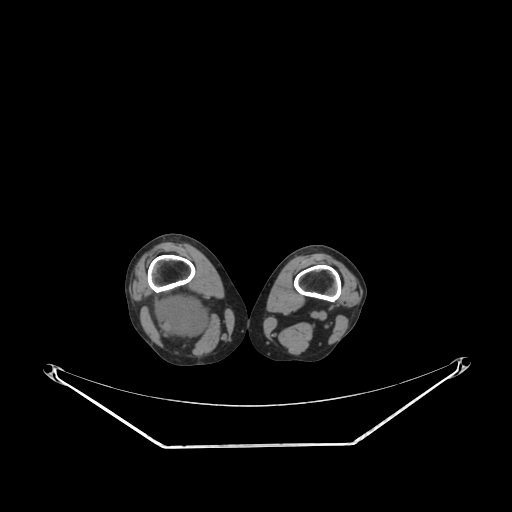
CT of an extremity soft-tissue mass (from a PET/CT study), one axial slice; slice 184 of 267 in the series (ordered by position); soft-tissue window (W 400 / L 40 HU); 512 × 512 image matrix, field of view 500 × 500 mm. Female patient. From the clinical record (not read from this slice): histological type: liposarcoma; site of the primary tumour: right thigh.
Structures marked on this image (expert contour drawn on MRI and transferred to this co-registered scan by the dataset authors):
- gross tumour volume (mass): bounding box [x1, y1, x2, y2] px = [151, 292, 211, 341]